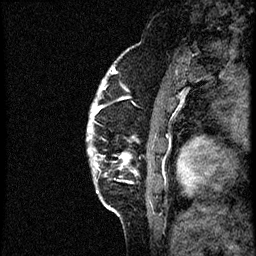
Breast MRI (dynamic contrast-enhanced), one sagittal slice; dynamic contrast-enhanced study with each time point stored as its own series, time point 2 of 3 at this slice position (early post-contrast, ordered by acquisition time); 1.5 T; TE 4.2 ms, TR 21.3 ms; 2 mm slice thickness; 256 × 256 image matrix, field of view 200 × 200 mm. Female patient, age 41 years. From the clinical record (not read from this slice): setting: breast cancer imaged before/during neoadjuvant chemotherapy; receptor status: HER2-positive.
Structures marked on this image (semi-automatic segmentation, software-assisted and operator-edited):
- analysis volume of interest (the breast-tissue region the enhancement analysis was run in; not a lesion): box from (x=86, y=73) to (x=177, y=205) px
- tumour enhancement mask (voxels above the 100 % enhancement threshold inside the analysis volume of interest): (x=88, y=84)–(x=125, y=157)